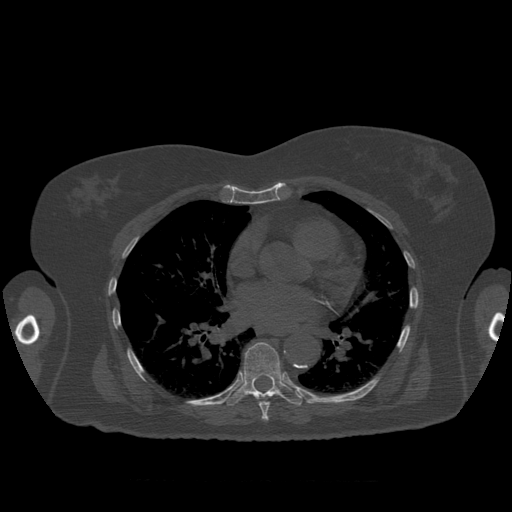
CT including the spine, one axial slice; position 385 of 399 along the scan axis; bone window (W 1800 / L 400 HU); 512 × 512 image matrix, field of view 404 × 404 mm. Patient age 81 years. From the clinical record (not read from this slice): primary cancer: renal.
Structures marked on this image (semi-automatically segmented with operator editing):
- T7 vertebra: box from (x=249, y=394) to (x=270, y=421) px
- T8 vertebra: (x=225, y=343)–(x=303, y=407)